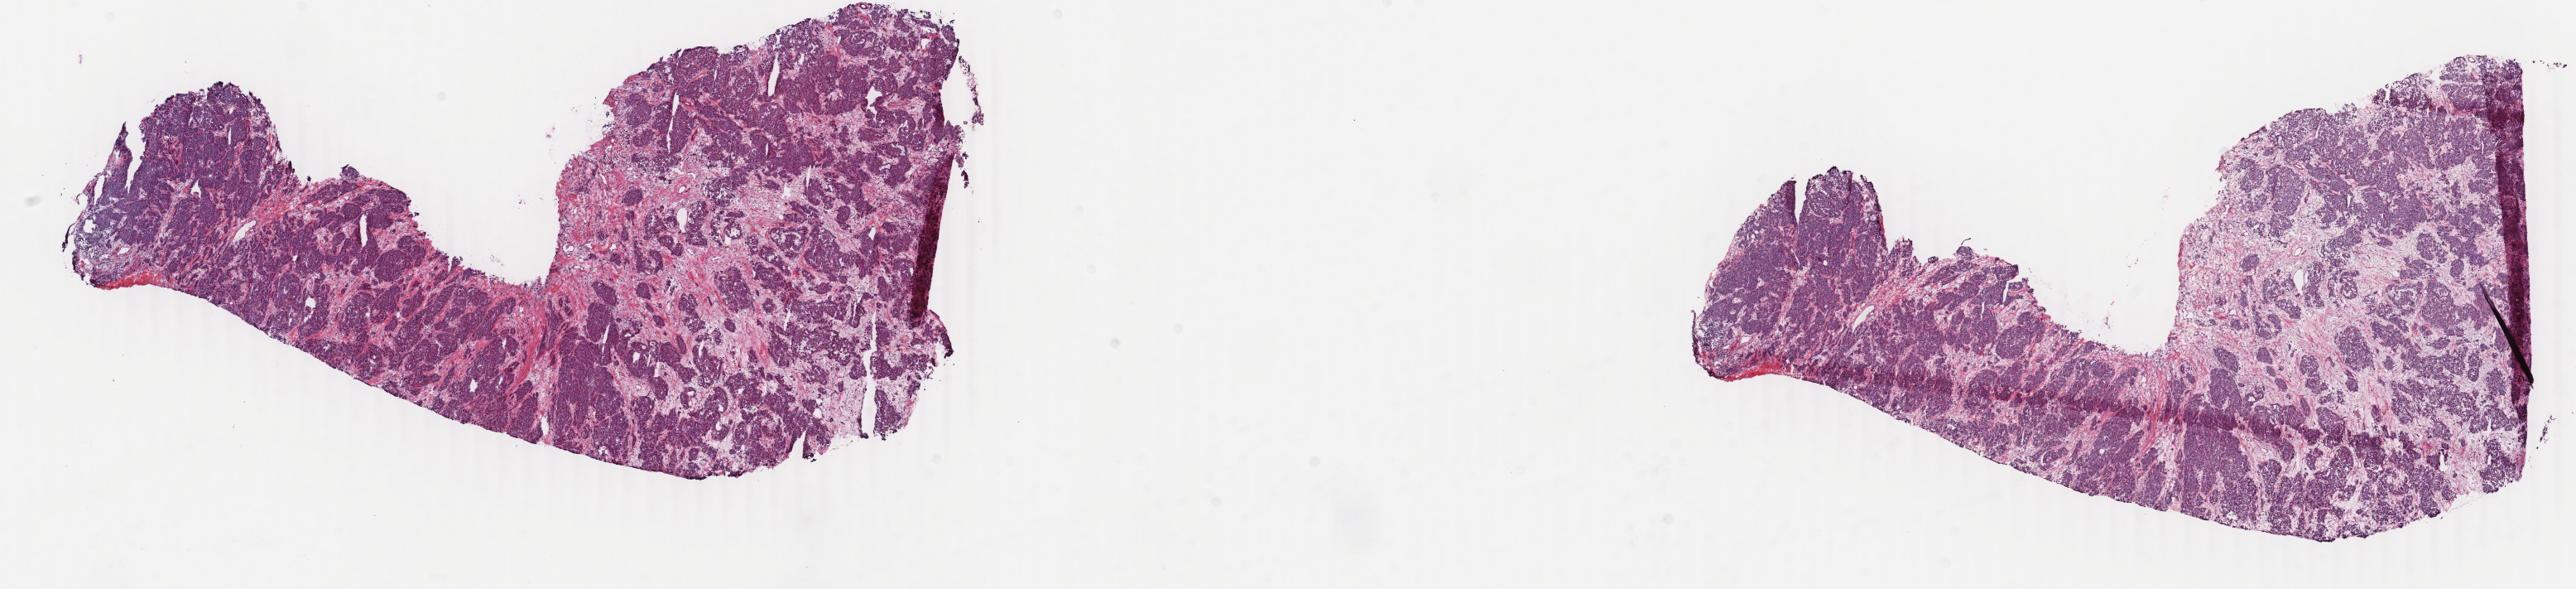
Digitized H&E tissue section (whole slide) — low-resolution overview of the scanned area, about 24.7 x 5.7 mm; frozen section; sample: primary tumour, breast. Patient: female, age at initial diagnosis 61 years. Pathologist review of this section (percent, as recorded): tumour cells 45%, tumour nuclei 85%, normal cells 0%, stromal cells 54%, necrosis 1%. Infiltration values recorded for this section: lymphocyte infiltration 2%, monocyte infiltration 1%, neutrophil infiltration 0%.
Histologic diagnosis: Infiltrating duct carcinoma, NOS. Lymph nodes positive (case pathology): 4 of 15 examined. AJCC pathologic stage: IIIA.